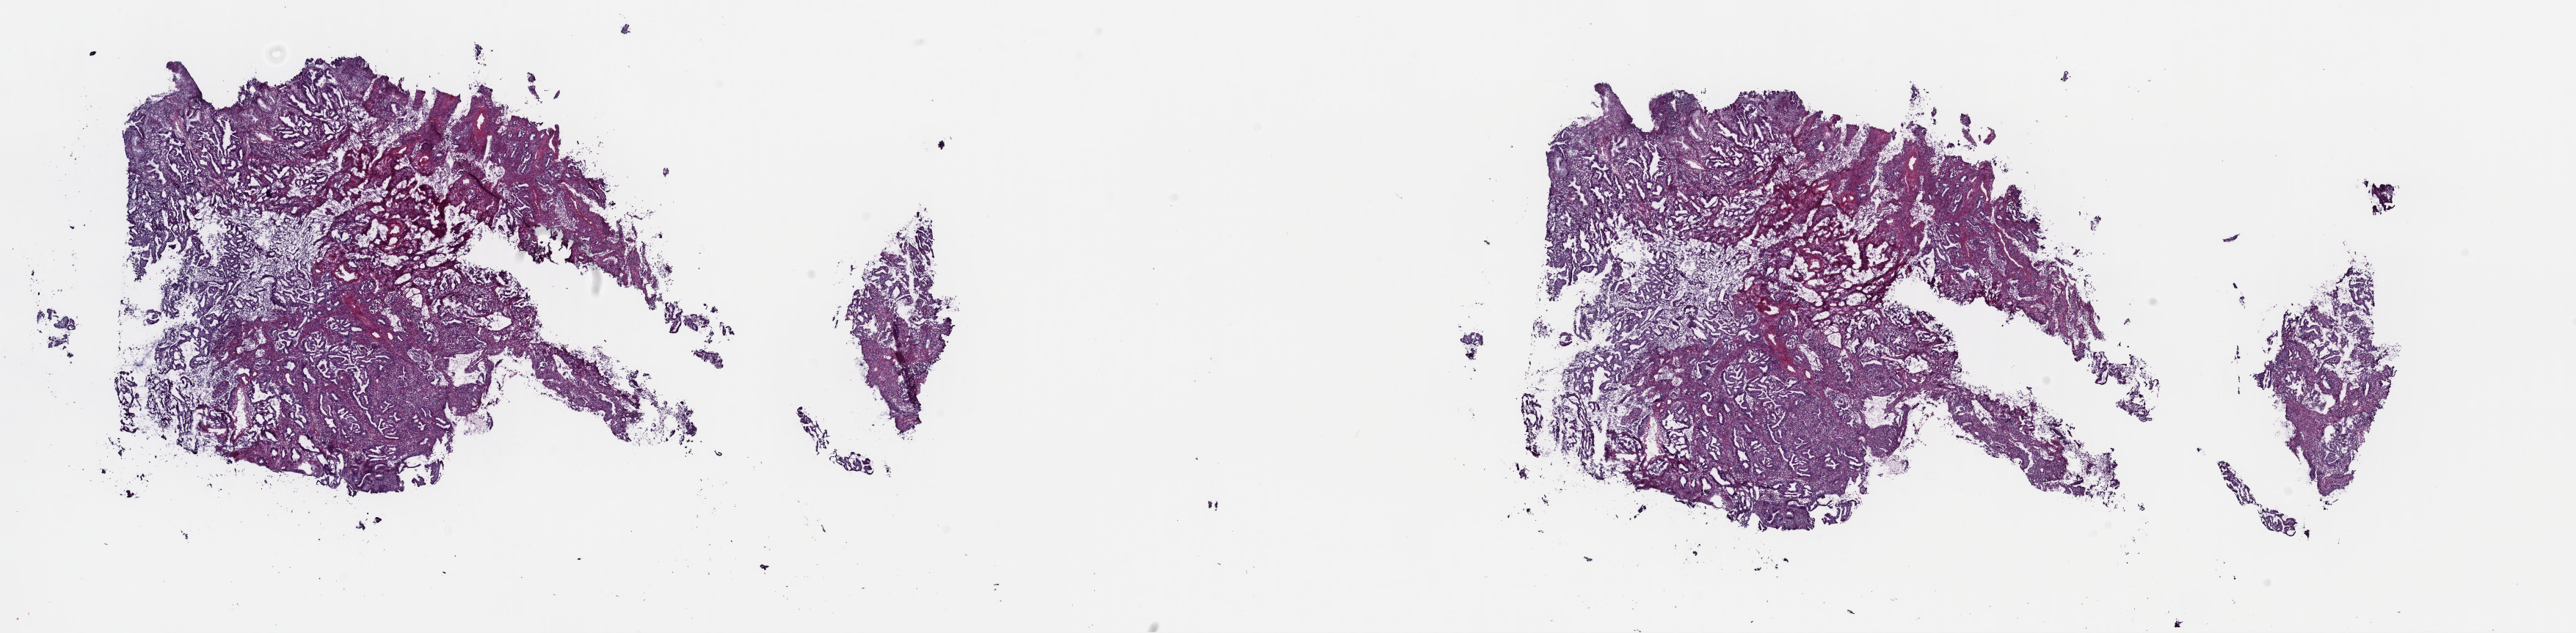
Whole-slide histology image, H&E, low-resolution overview of the scanned area, about 27.7 x 6.8 mm, frozen section, cervix, primary tumour sample. Patient: female, age at initial diagnosis 24 years. Histologic grade: G2 (moderately differentiated). Composition of this section per pathologist review: tumour cells 80%, tumour nuclei 65%, normal cells 15%, stromal cells 0%, necrosis 5%. Inflammatory infiltration, as recorded: lymphocyte infiltration 15%, monocyte infiltration 2%, neutrophil infiltration 0%.
* histologic diagnosis: Mucinous adenocarcinoma, endocervical type
* FIGO stage: IB2